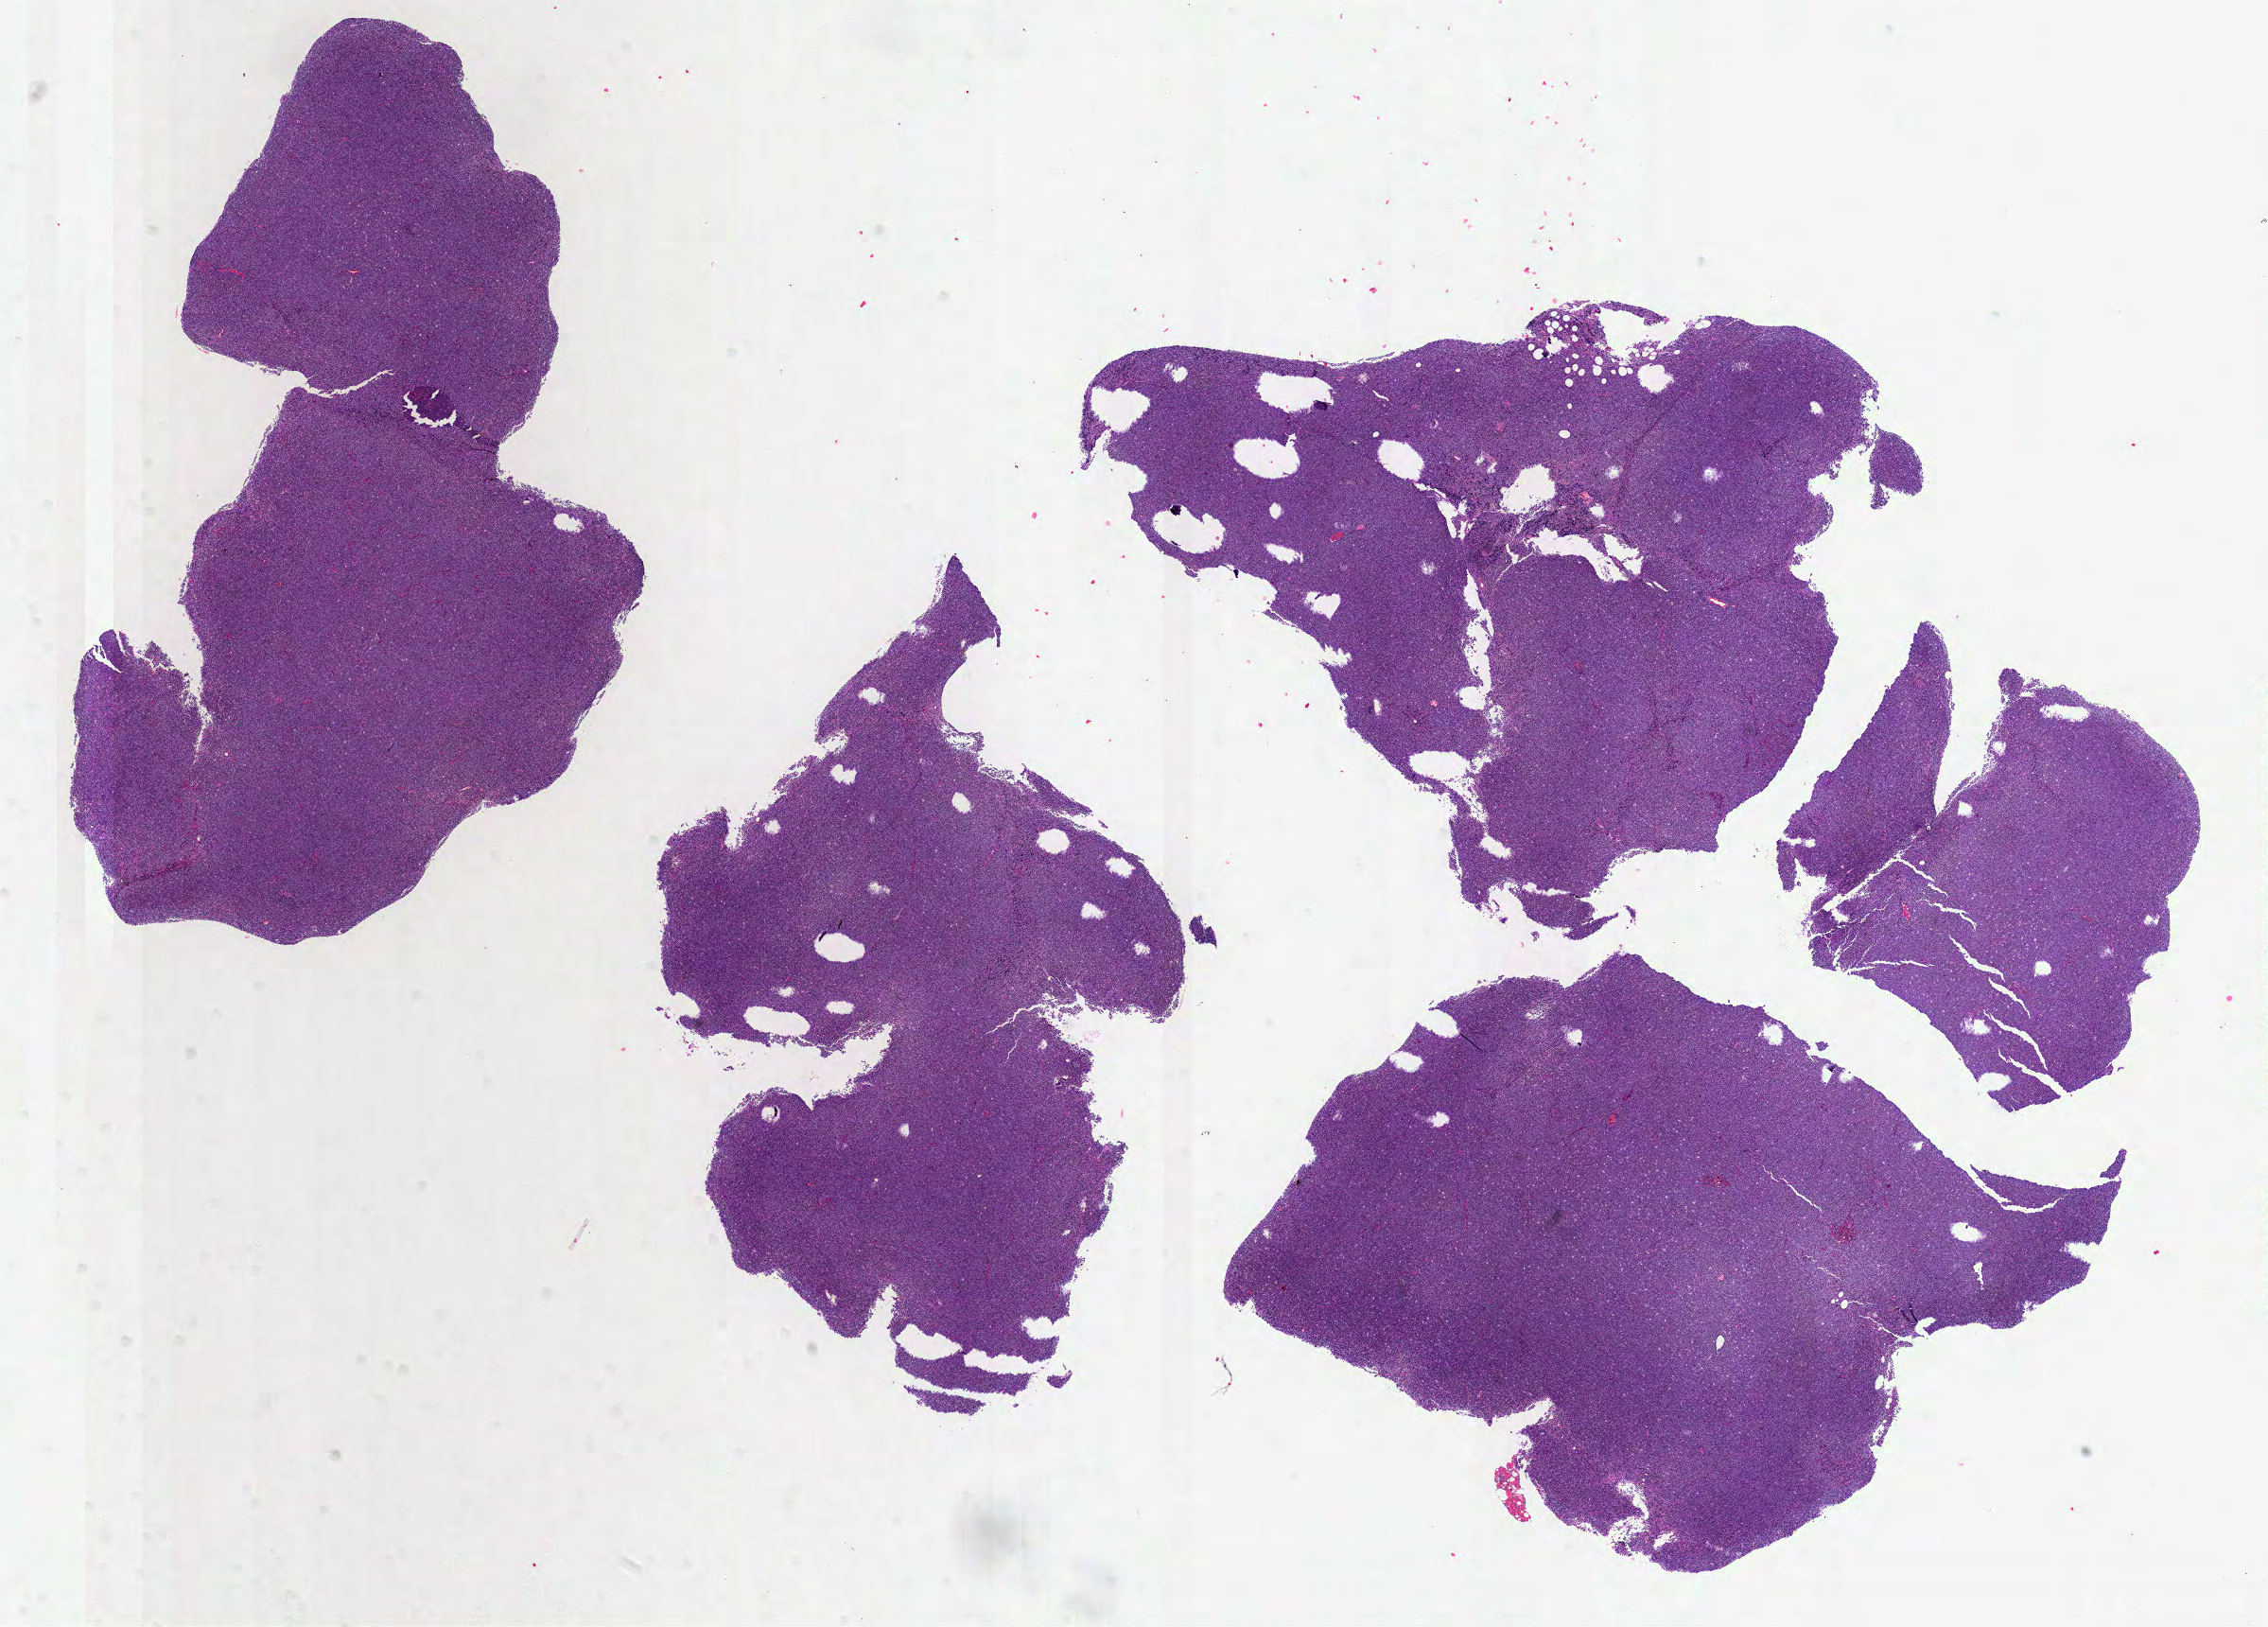
Digitized Hematoxylin and eosin (H&E) stained tissue section (whole slide), low-resolution overview of the scanned area, about 19.3 x 13.9 mm (slide scanned at 40x), FFPE section, primary tumour sample from the lymphoid tissue. Patient: female, age at initial diagnosis 38 years.
Histologic diagnosis: Diffuse large B-cell lymphoma, NOS (lymph nodes of head, face and neck).